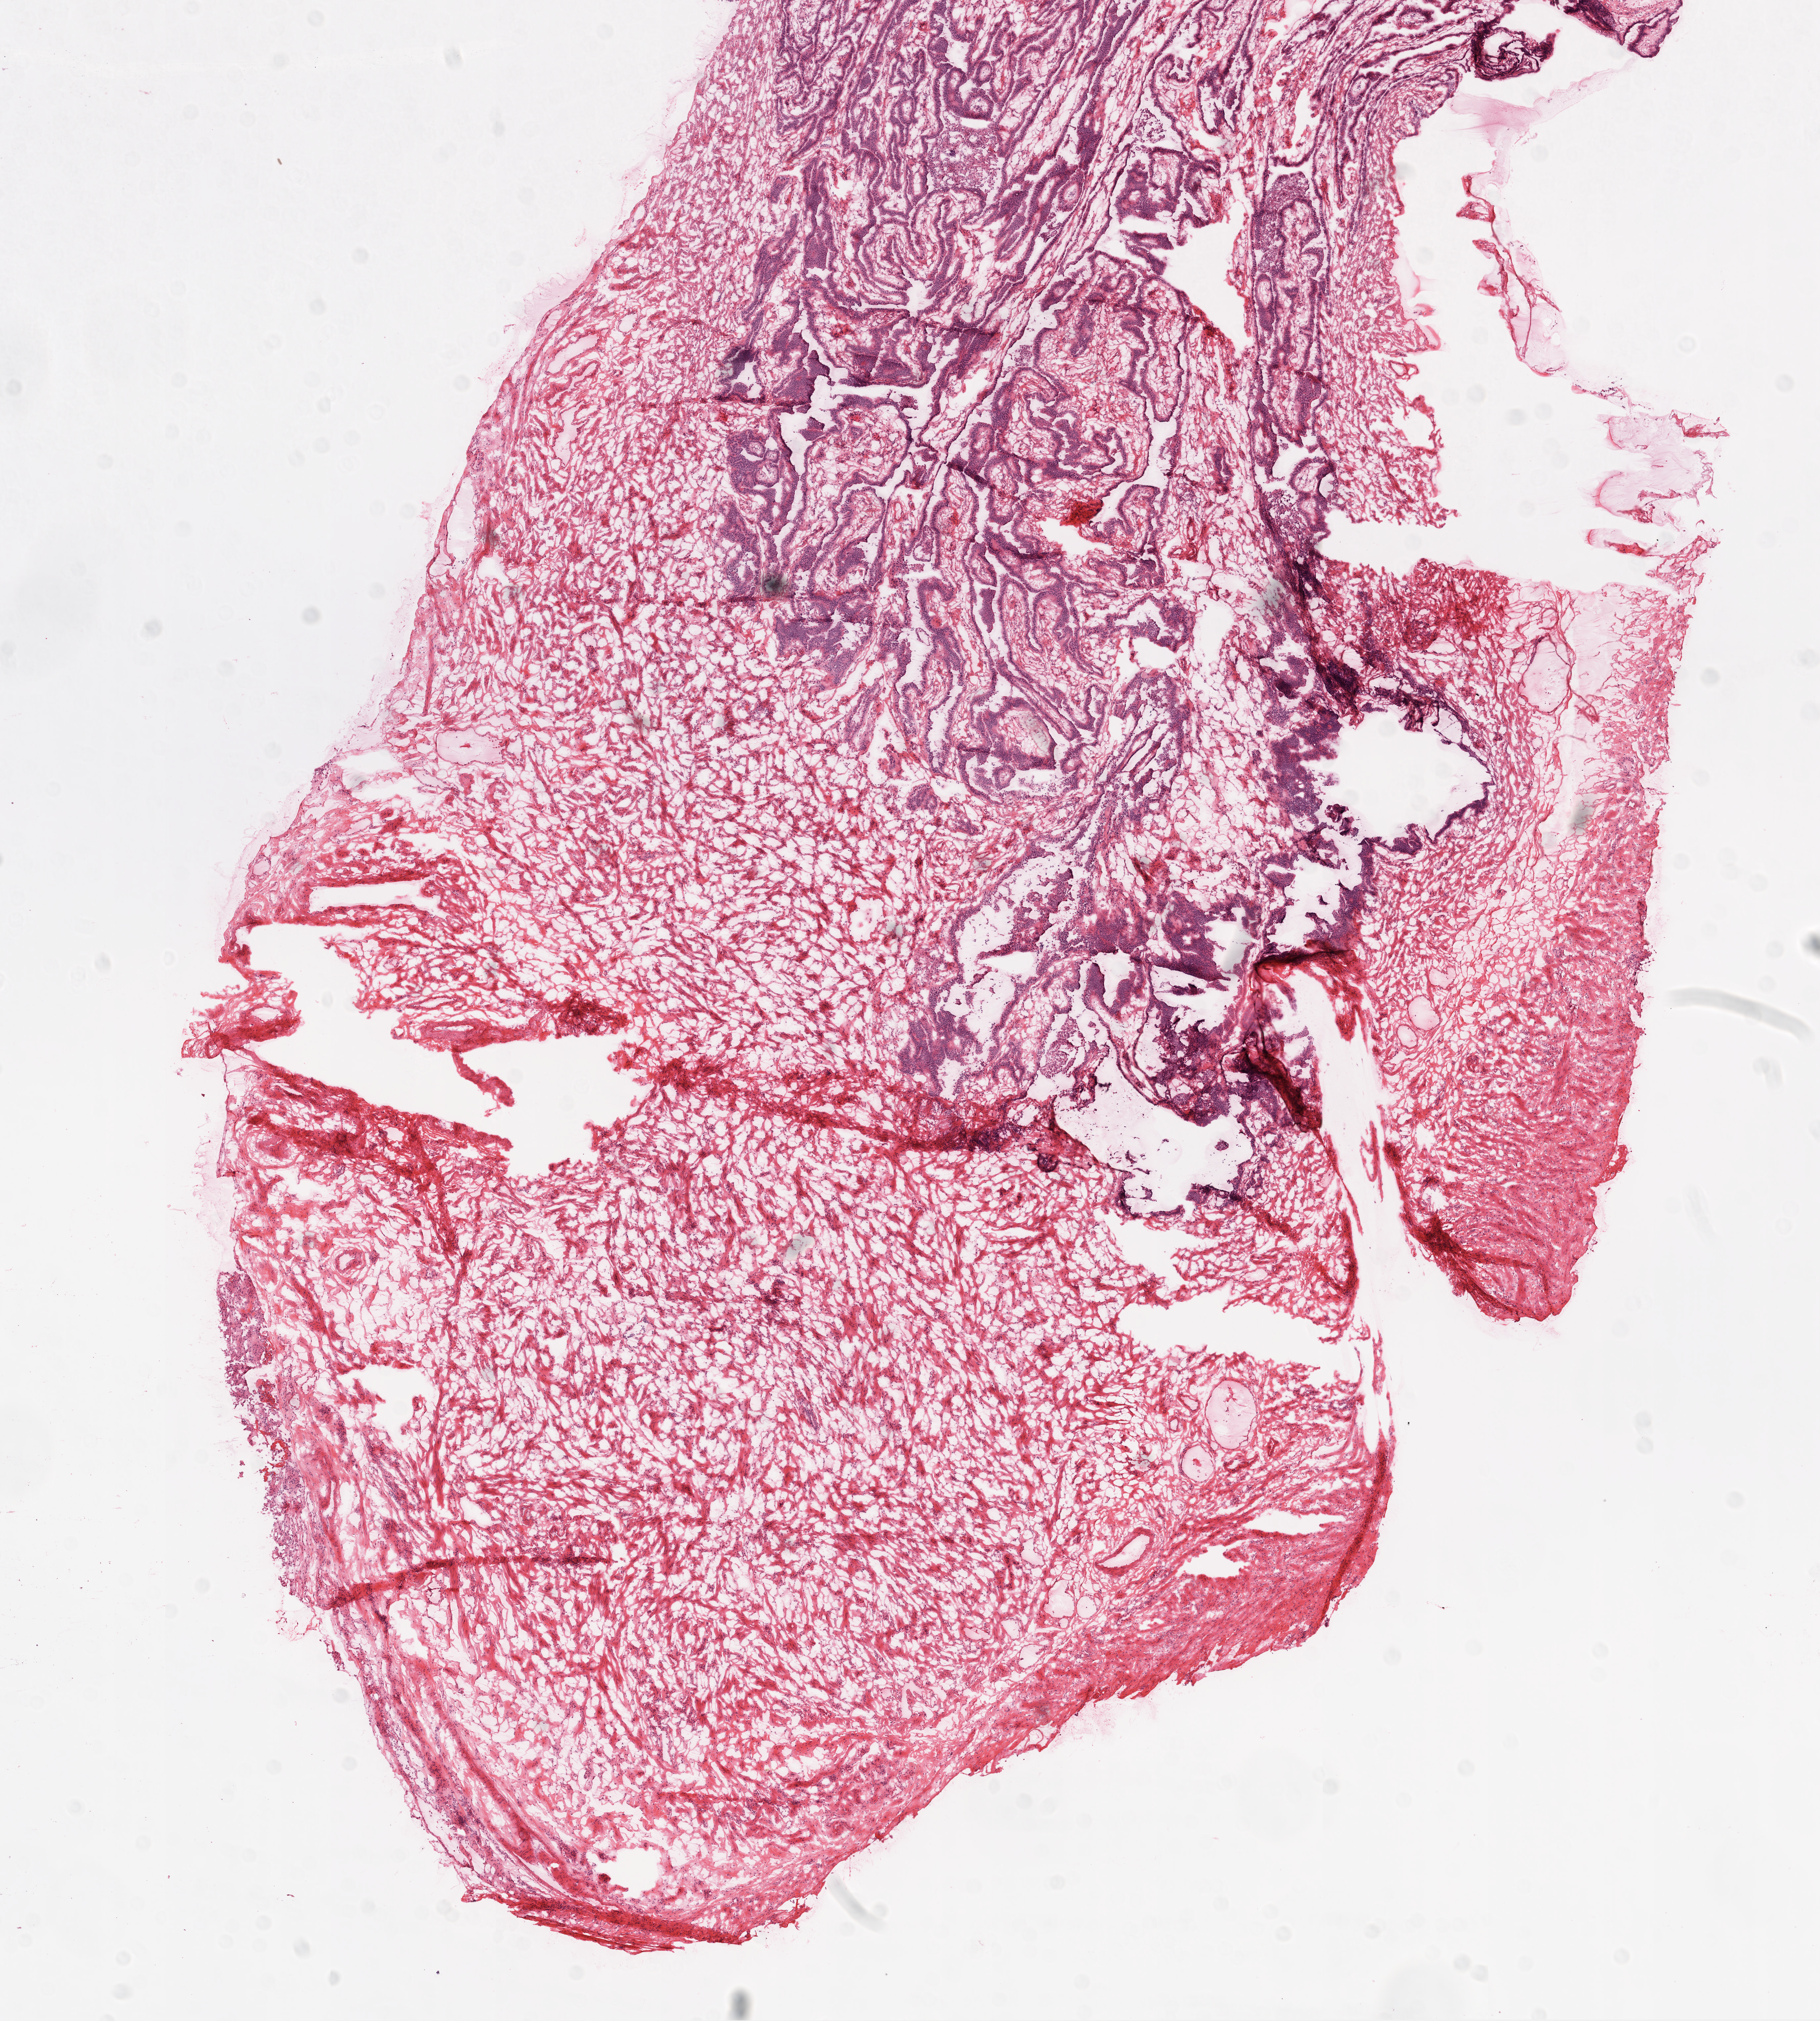
H&E whole-slide image — shown as a low-resolution overview of the whole scanned area (about 11.0 x 12.2 mm). Frozen section from the top of the tissue portion. Solid tissue normal (non-tumour tissue) sample from the ovary. Patient: female, age at initial diagnosis 43 years.
This section: solid tissue normal sample (biorepository sample class). Patient diagnosis: Serous cystadenocarcinoma, NOS.